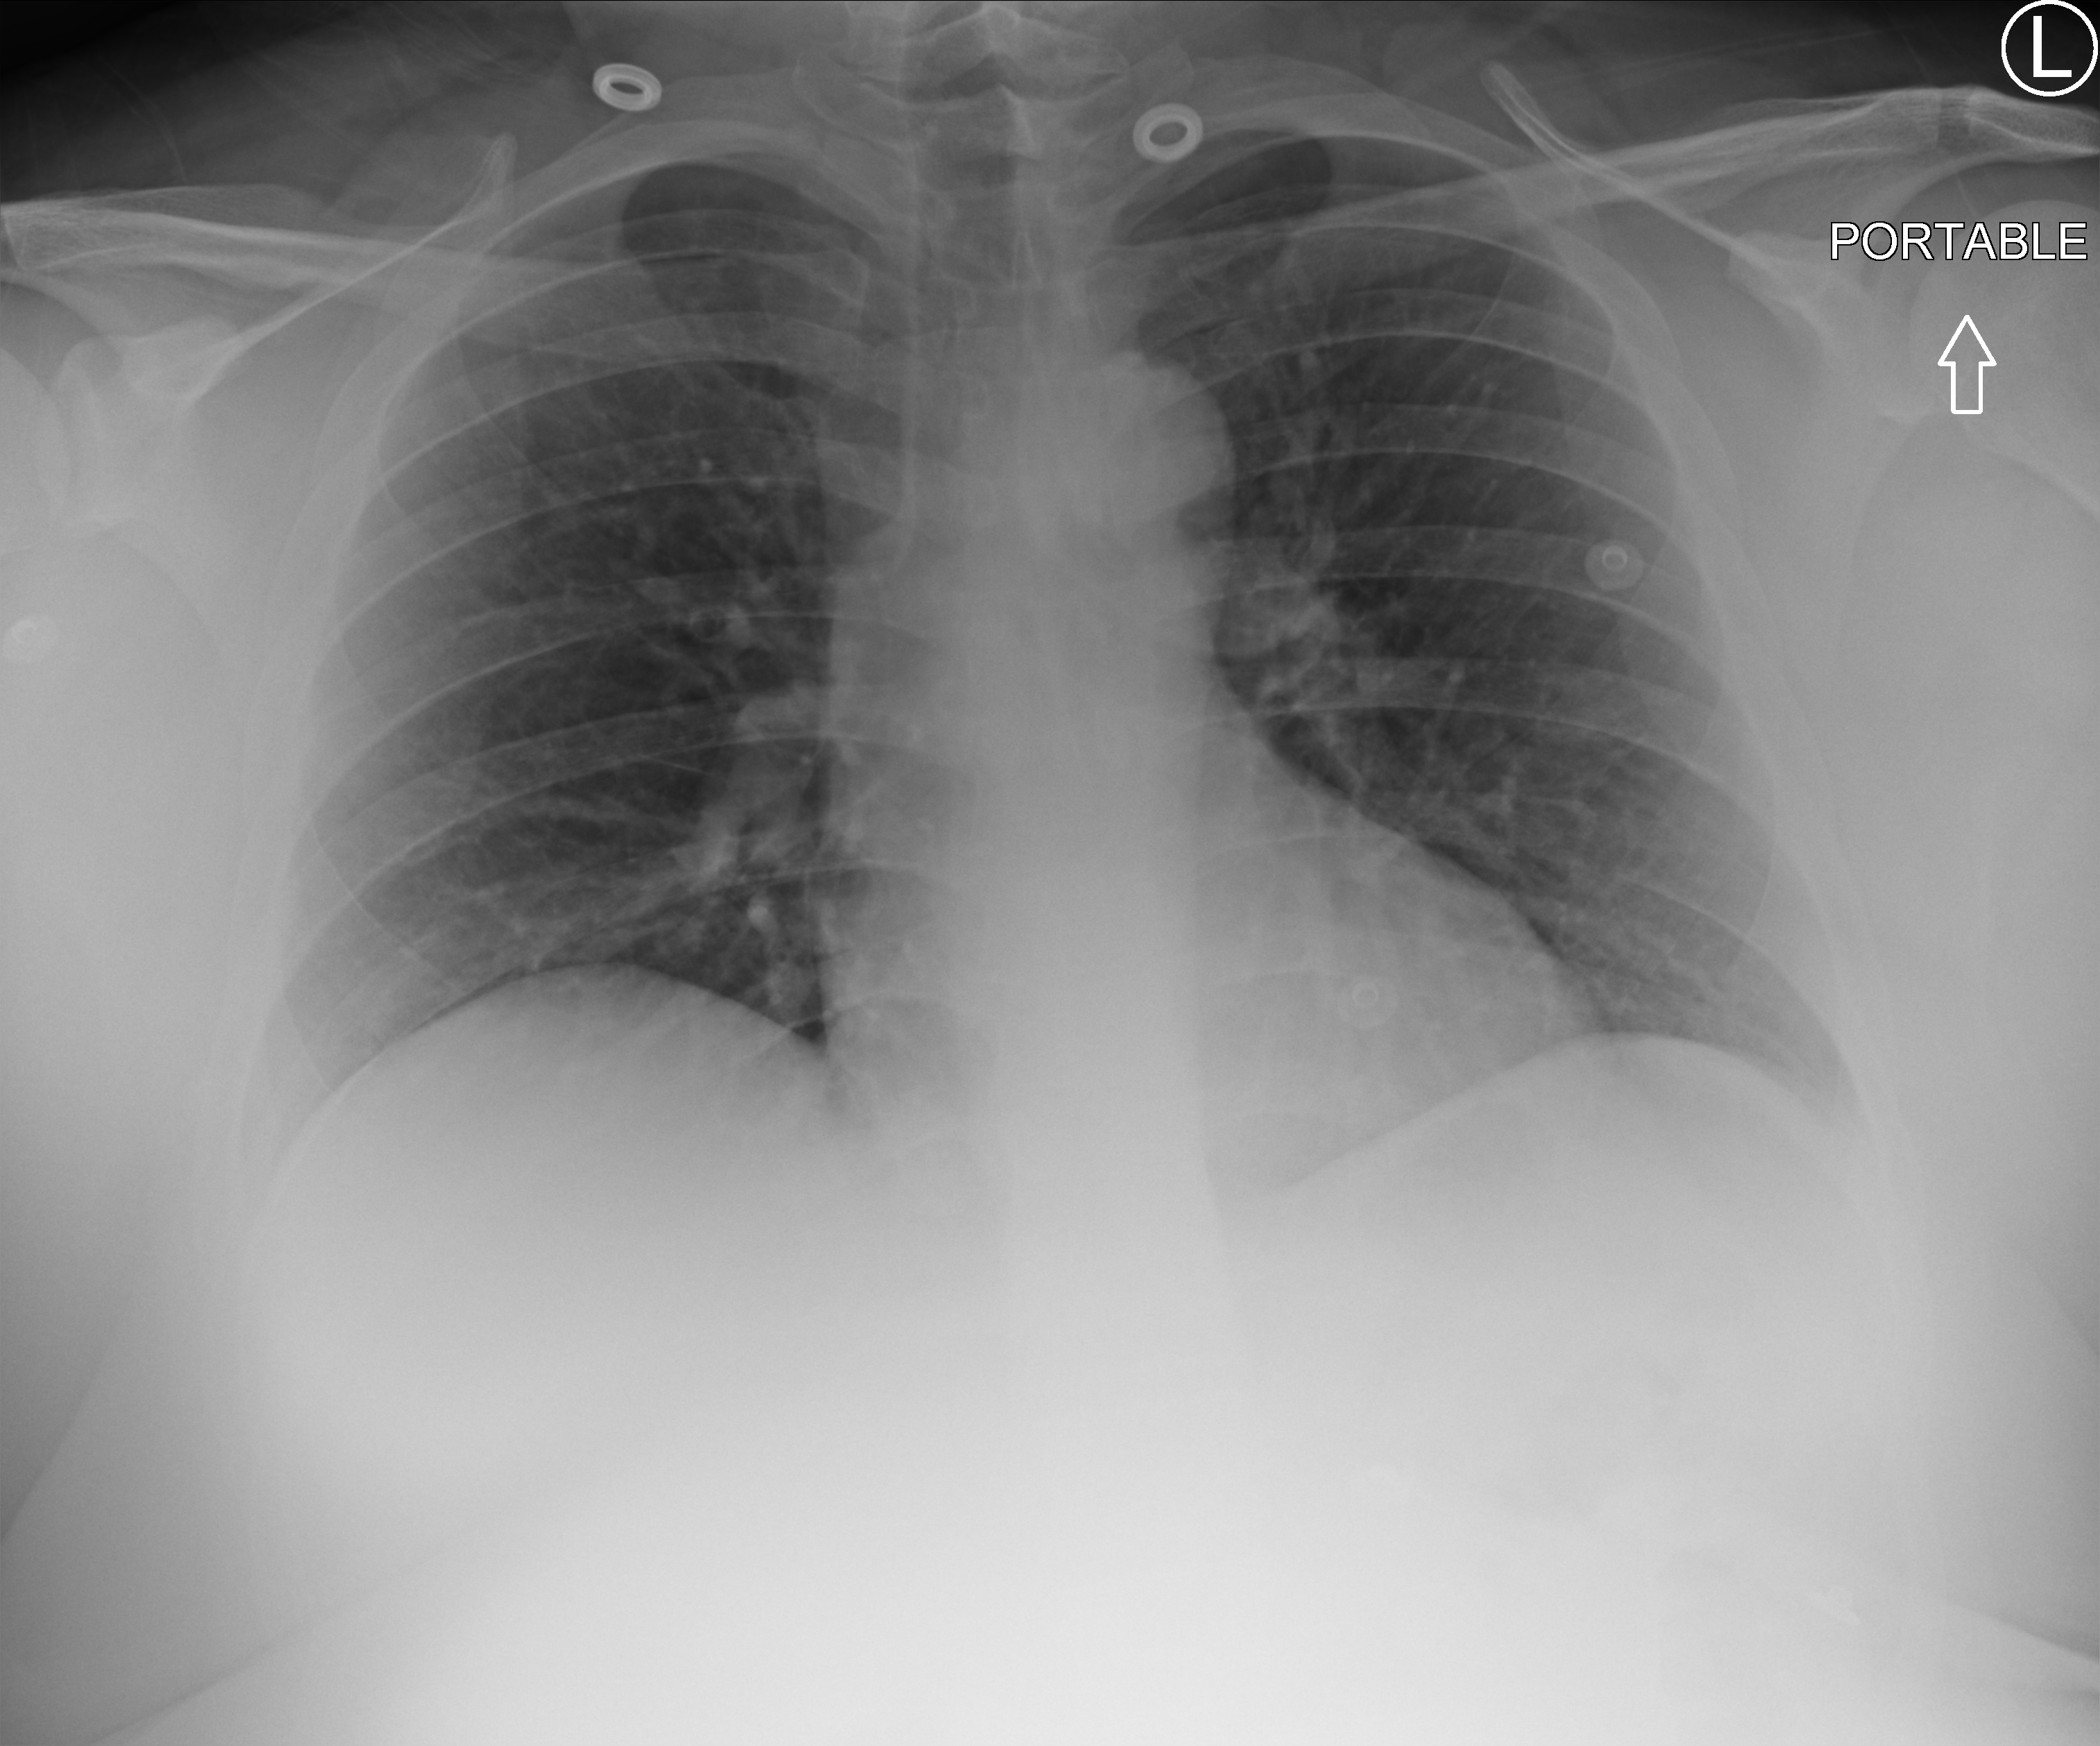
Chest X-ray (portable); anteroposterior (AP) projection. Male patient hospitalised with COVID-19, age 18–59 years.
Admission-level facts for this patient (not findings on this image; timing relative to this image not recorded):
- mechanically ventilated during this hospital stay: no
- admitted to intensive care during this hospital stay: no